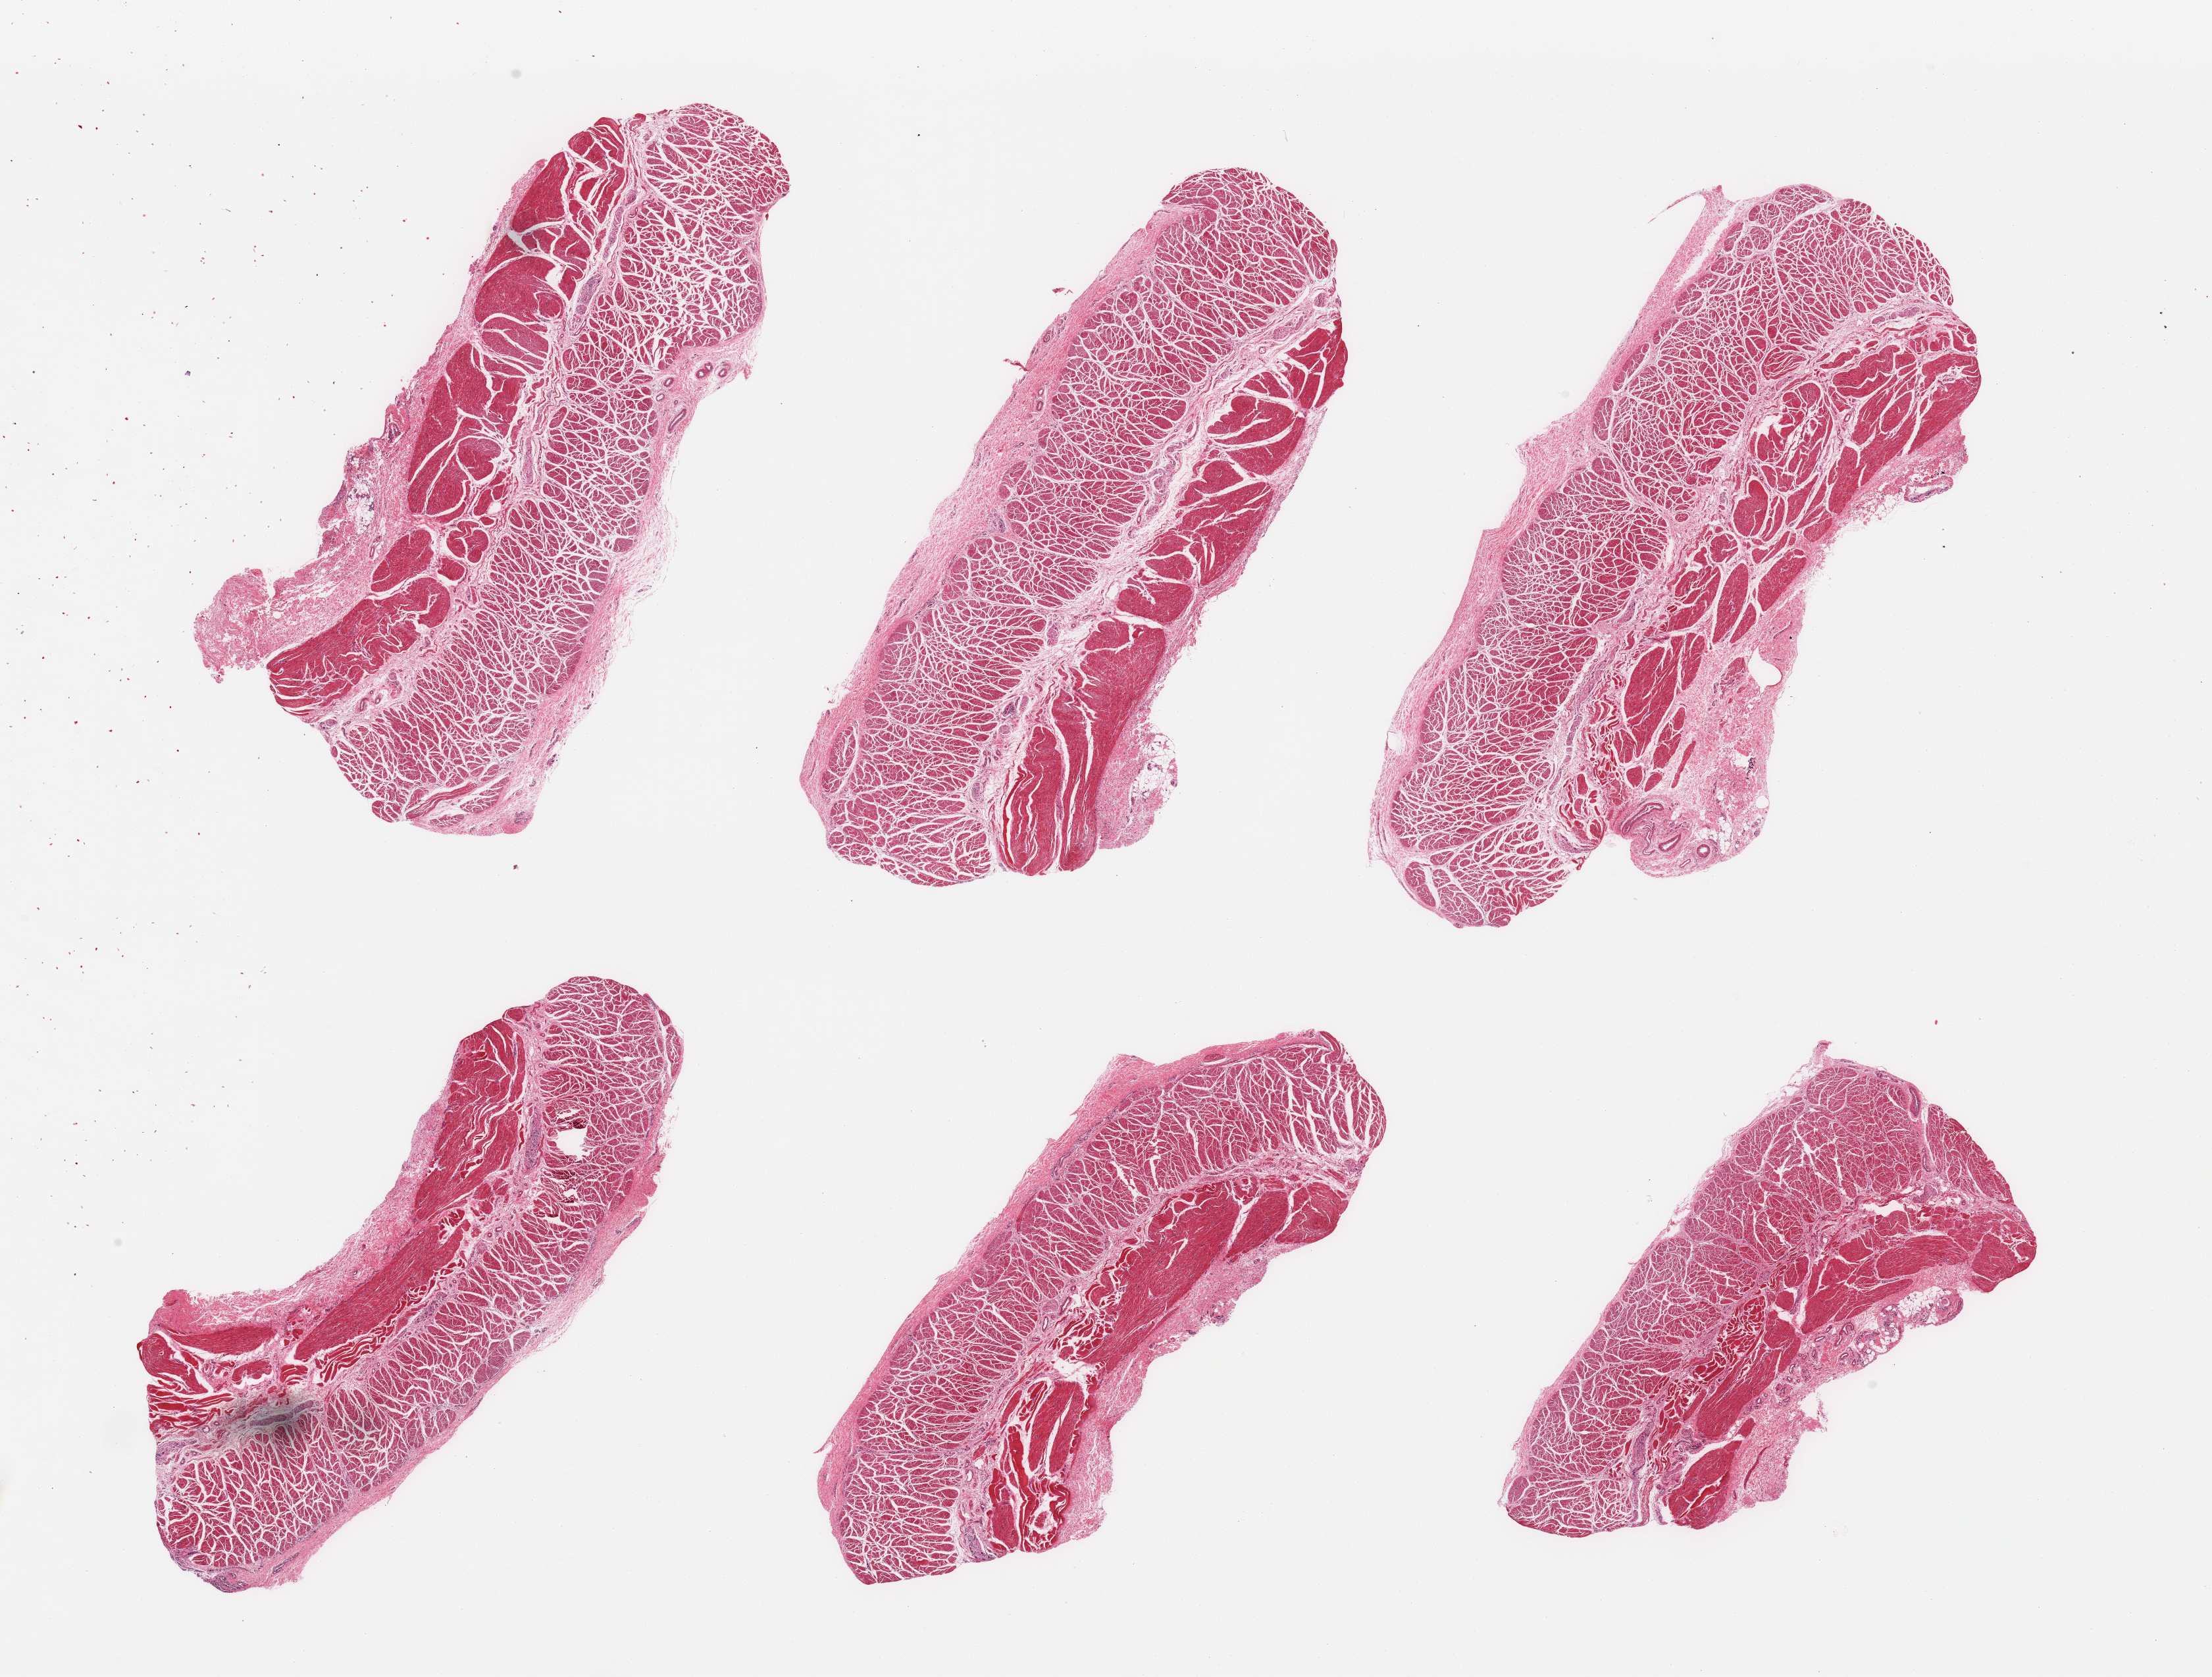
Digitized H&E-stained section, brightfield — a low-resolution overview of the entire scanned area, about 26.6 x 20.2 mm, PAXgene-fixed, paraffin-embedded tissue, section of esophageal muscle (target tissue), tissue donor sample. Donor: female.
* pathologist's review note for this sample: 6 pieces; well dissected muscularis propria